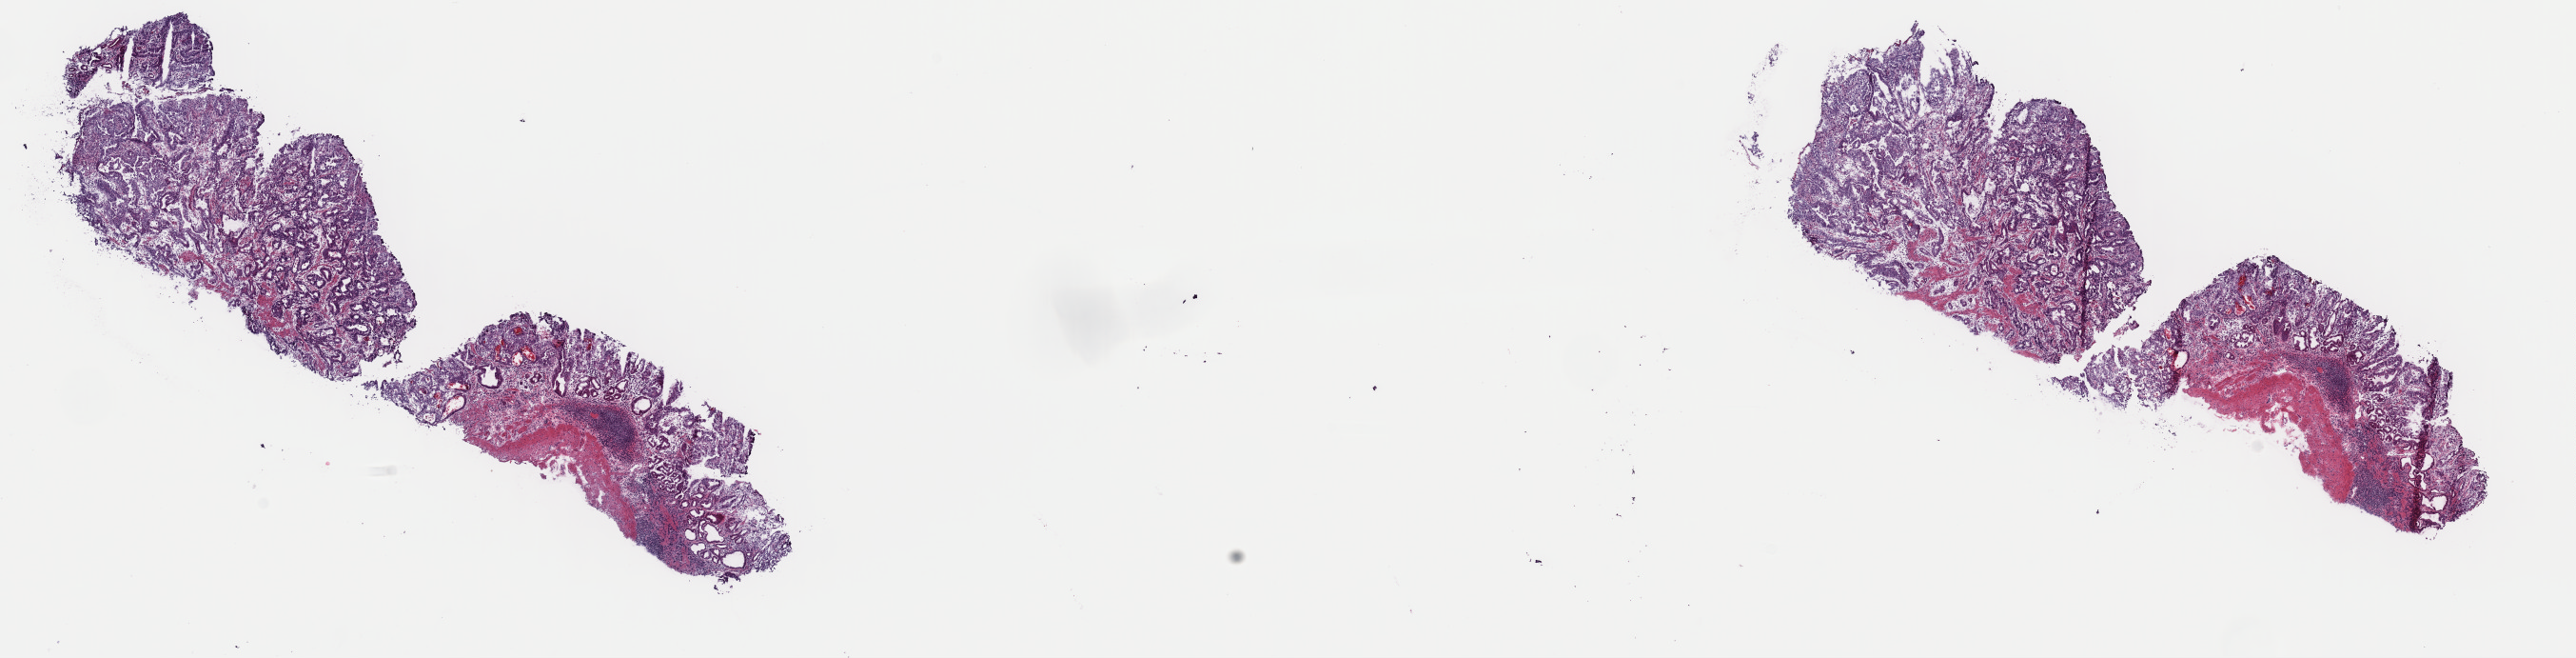
Digitized H&E tissue section (whole slide) — low-resolution overview of the scanned area, about 21.4 x 5.5 mm (from a 40x scan); frozen section from the top of the tissue portion; sample: primary tumour, stomach. Patient: male, age at initial diagnosis 61 years. Histologic grade: G2 (moderately differentiated). Slide review estimates, as recorded: tumour cells 80%, tumour nuclei 65%, normal cells 20%, stromal cells 0%, necrosis 0%. Infiltration values recorded for this section: lymphocyte infiltration 8%, monocyte infiltration 1%, neutrophil infiltration 1%.
Pathologic diagnosis: Adenocarcinoma, NOS. AJCC pathologic stage: IIA (7th edition).